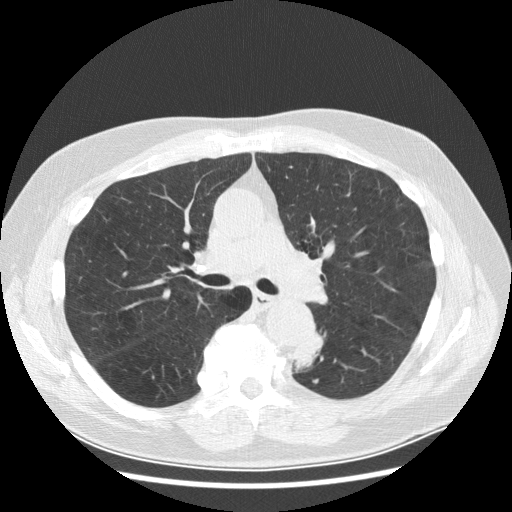
Low-dose screening chest CT, one axial slice; position 177 of 282 along the scan axis; reconstruction kernel STANDARD; 120 kVp; lung window (W 1500 / L -600 HU); 512 × 512 image matrix, field of view 370 × 370 mm.
Structures marked on this image (expert manual segmentation):
- lesion 1 (tumor, lower lobe of left lung): bounding box [x1, y1, x2, y2] px = [293, 333, 326, 373]